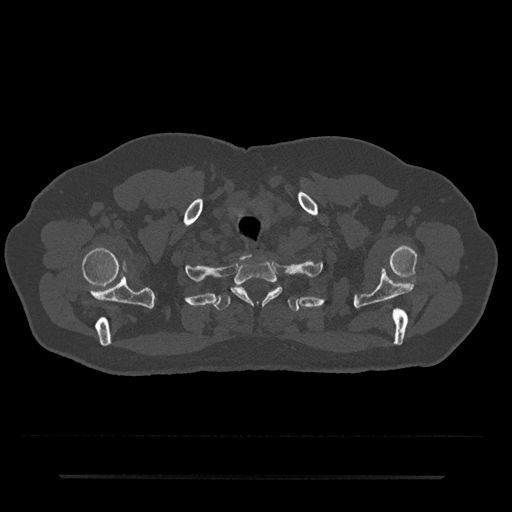
CT including the spine, one axial slice. Slice 632 of 797 in the series (ordered by position). Bone window (W 1800 / L 400 HU). 512 × 512 image matrix, field of view 437 × 437 mm. Patient: male, 69 years. Case-level facts recorded for this patient, not image findings: primary cancer: prostate.
Outlined on this slice (semi-automatically segmented with operator editing):
- T1 vertebra: box from (x=231, y=261) to (x=282, y=304) px
- T2 vertebra: (x=215, y=287)–(x=300, y=312)